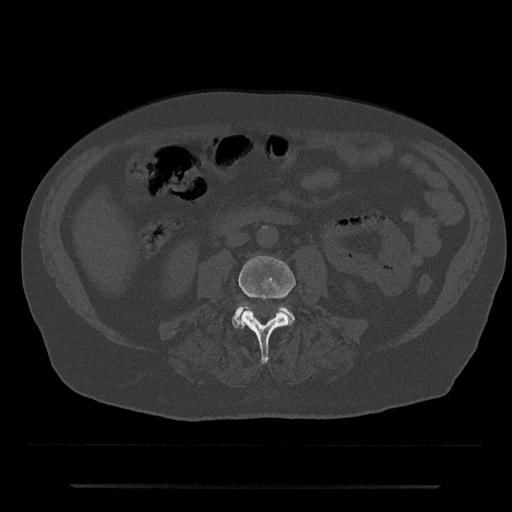
CT including the spine, one axial slice; slice 393 of 797 in the series (ordered by position); reconstruction kernel Br40s/3; bone window (W 1800 / L 400 HU); 512 × 512 image matrix. Patient: male, 80 years. Case-level facts recorded for this patient, not image findings: primary cancer: prostate.
Annotated regions visible in this slice (semi-automatic segmentation, software-assisted and operator-edited):
- L3 vertebra: box from (x=238, y=256) to (x=296, y=364) px
- L4 vertebra: (x=232, y=305)–(x=295, y=328)